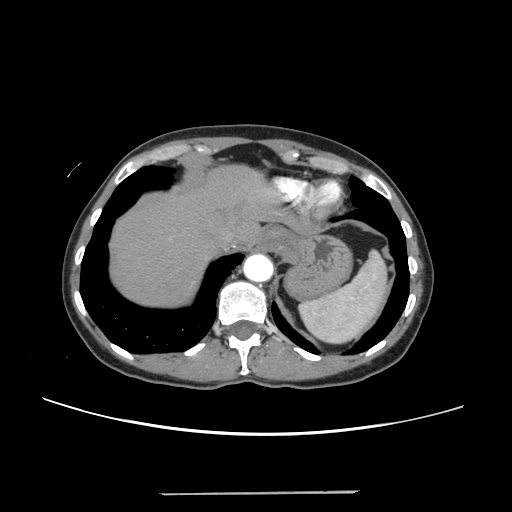
Contrast-enhanced abdominal CT, one axial slice. Slice 209 of 240 in the series (ordered by position). Intravenous contrast given. Soft-tissue window (W 400 / L 40 HU). 1.25 mm slice thickness. 512 × 512 image matrix, field of view 371 × 371 mm. Female patient, age 60 years. From the clinical record (not read from this slice): diagnosis: colorectal cancer liver metastases, imaged before liver resection; multiple liver metastases: no; largest metastasis: 1.5 cm; disease in both lobes: no.
Annotated regions visible in this slice (expert manual segmentation):
- hepatic veins: bounding box [x1, y1, x2, y2] px = [221, 226, 249, 242]
- liver: [110, 167, 276, 307]
- planned liver remnant (the part of the liver to remain after resection): [110, 166, 276, 307]